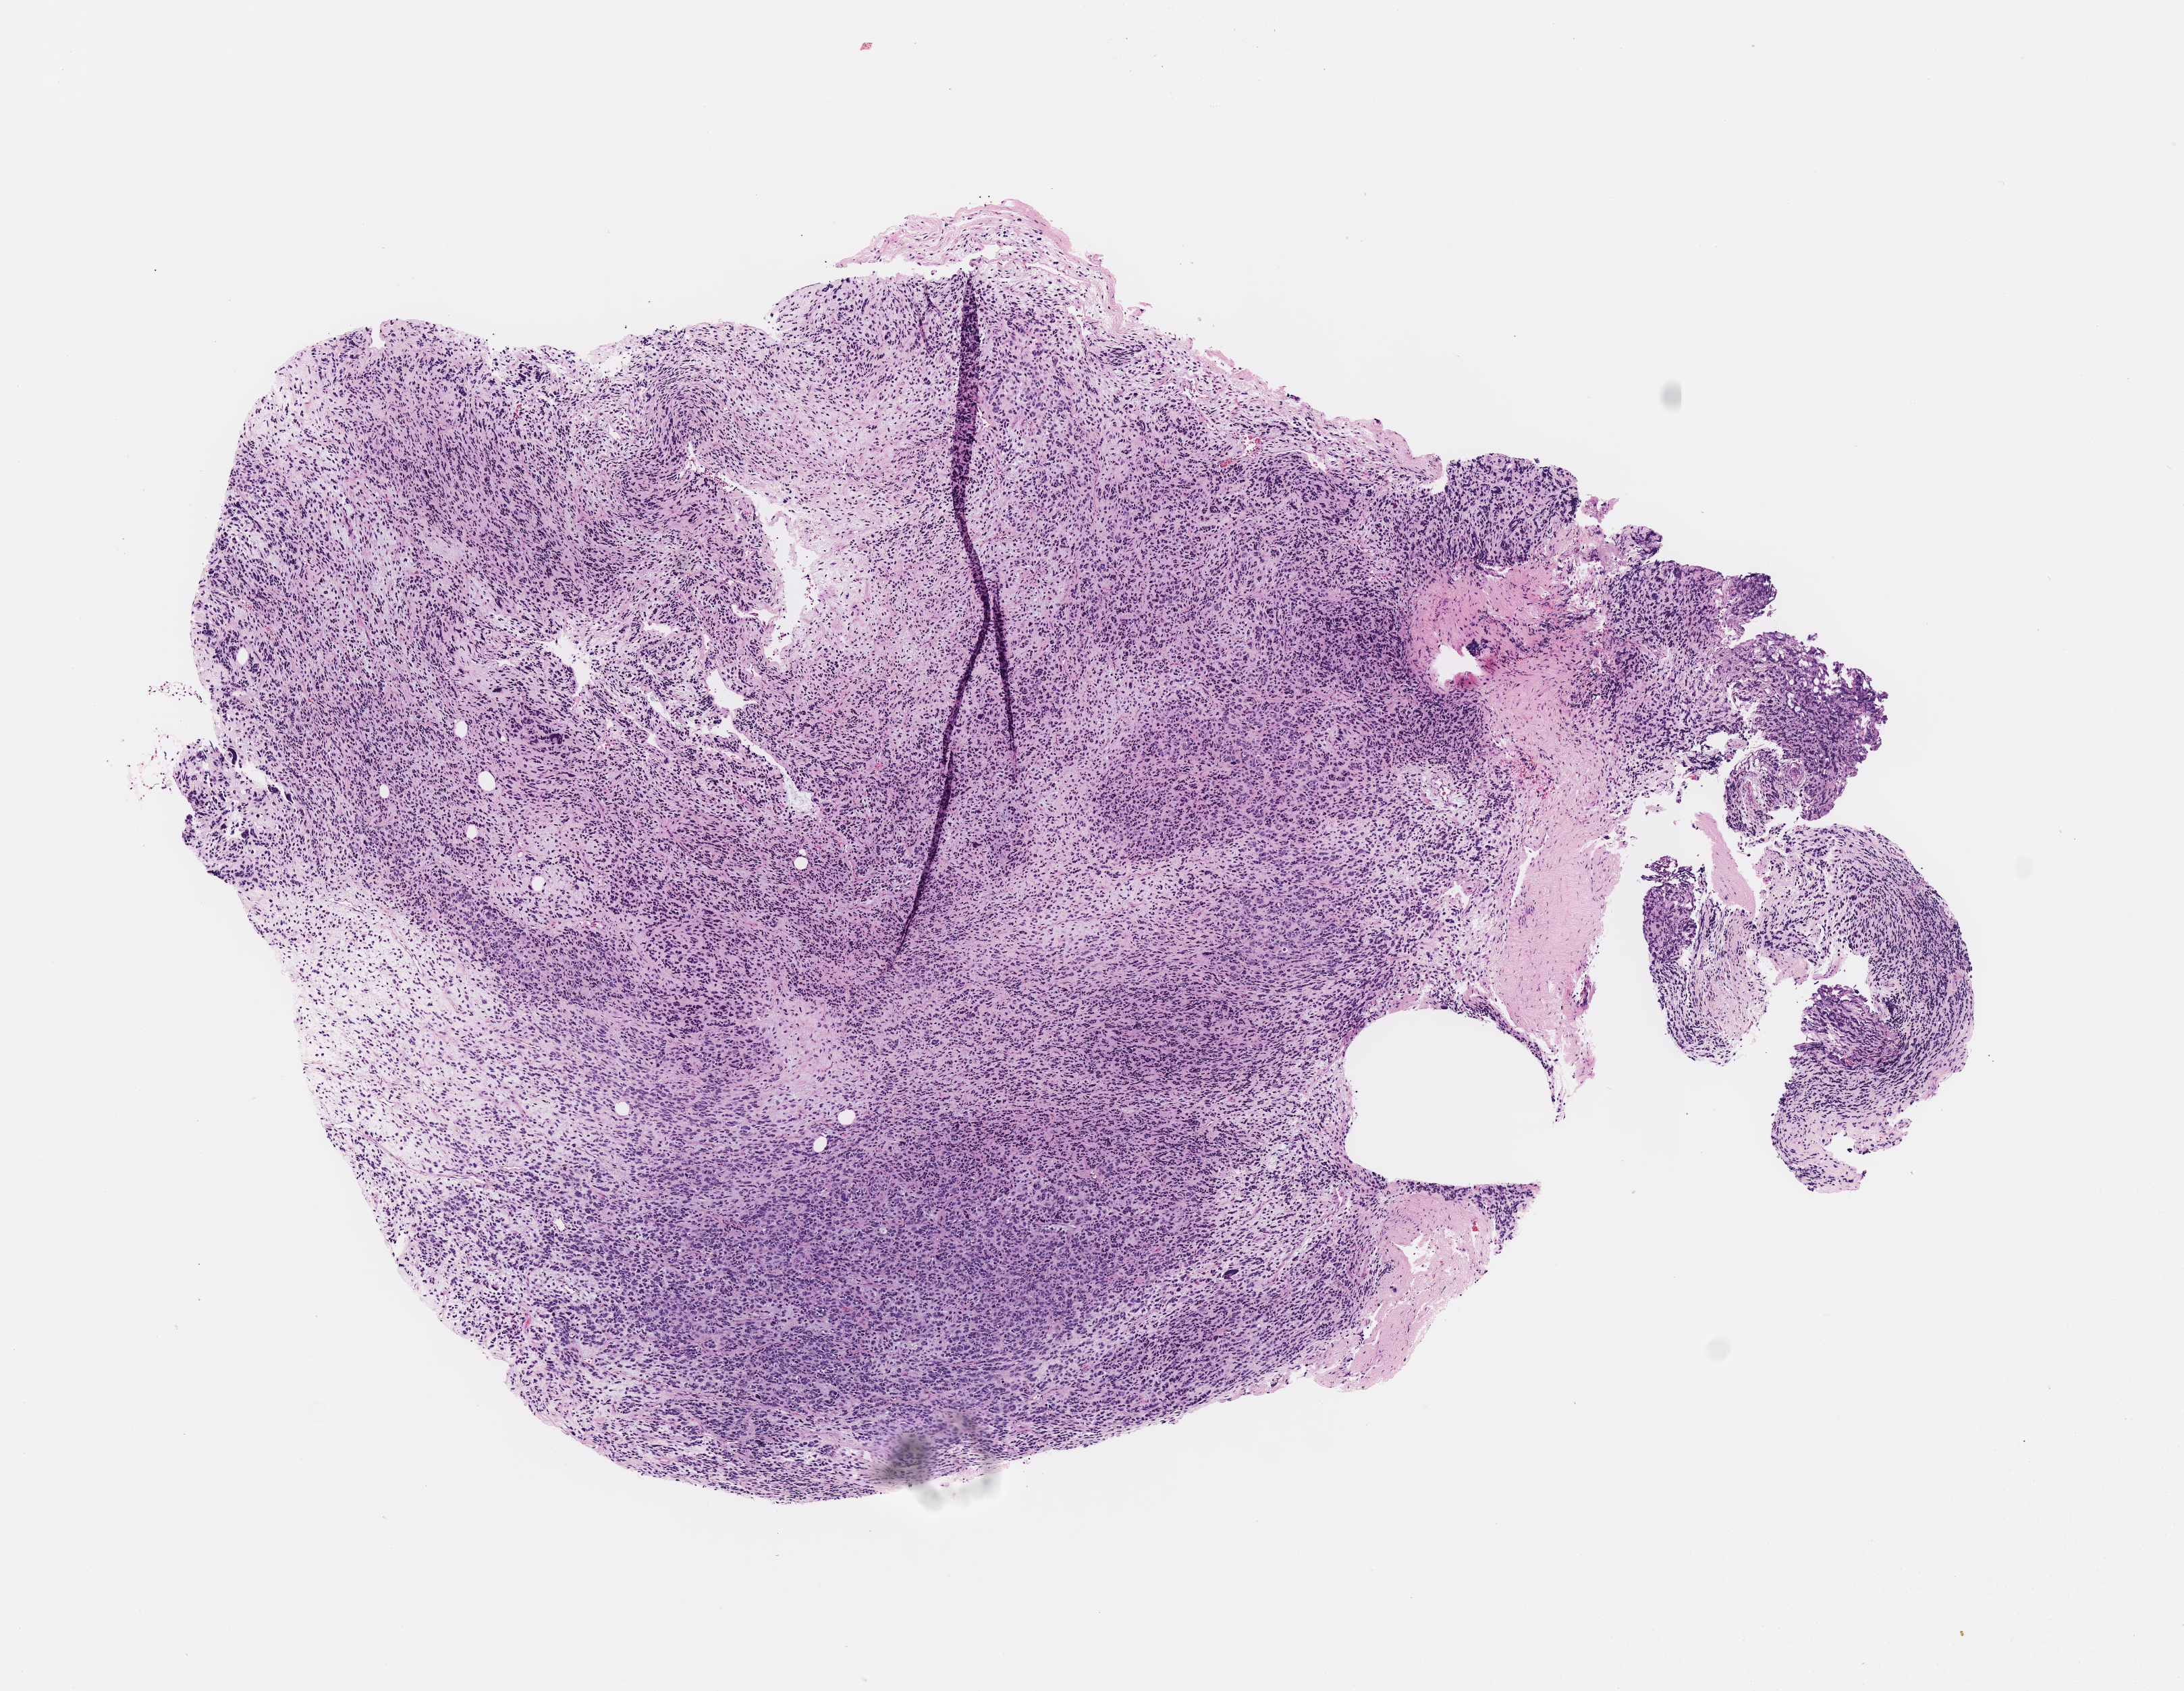
Whole-slide image, H&E stain of tumor tissue, low-resolution overview of the scanned area, about 6.5 x 5.1 mm; FFPE section; site: right thigh. Male patient, age at diagnosis 5.0 years.
Diagnosis: rhabdomyosarcoma; histological classification: spindle cell rhabdomyosarcoma.